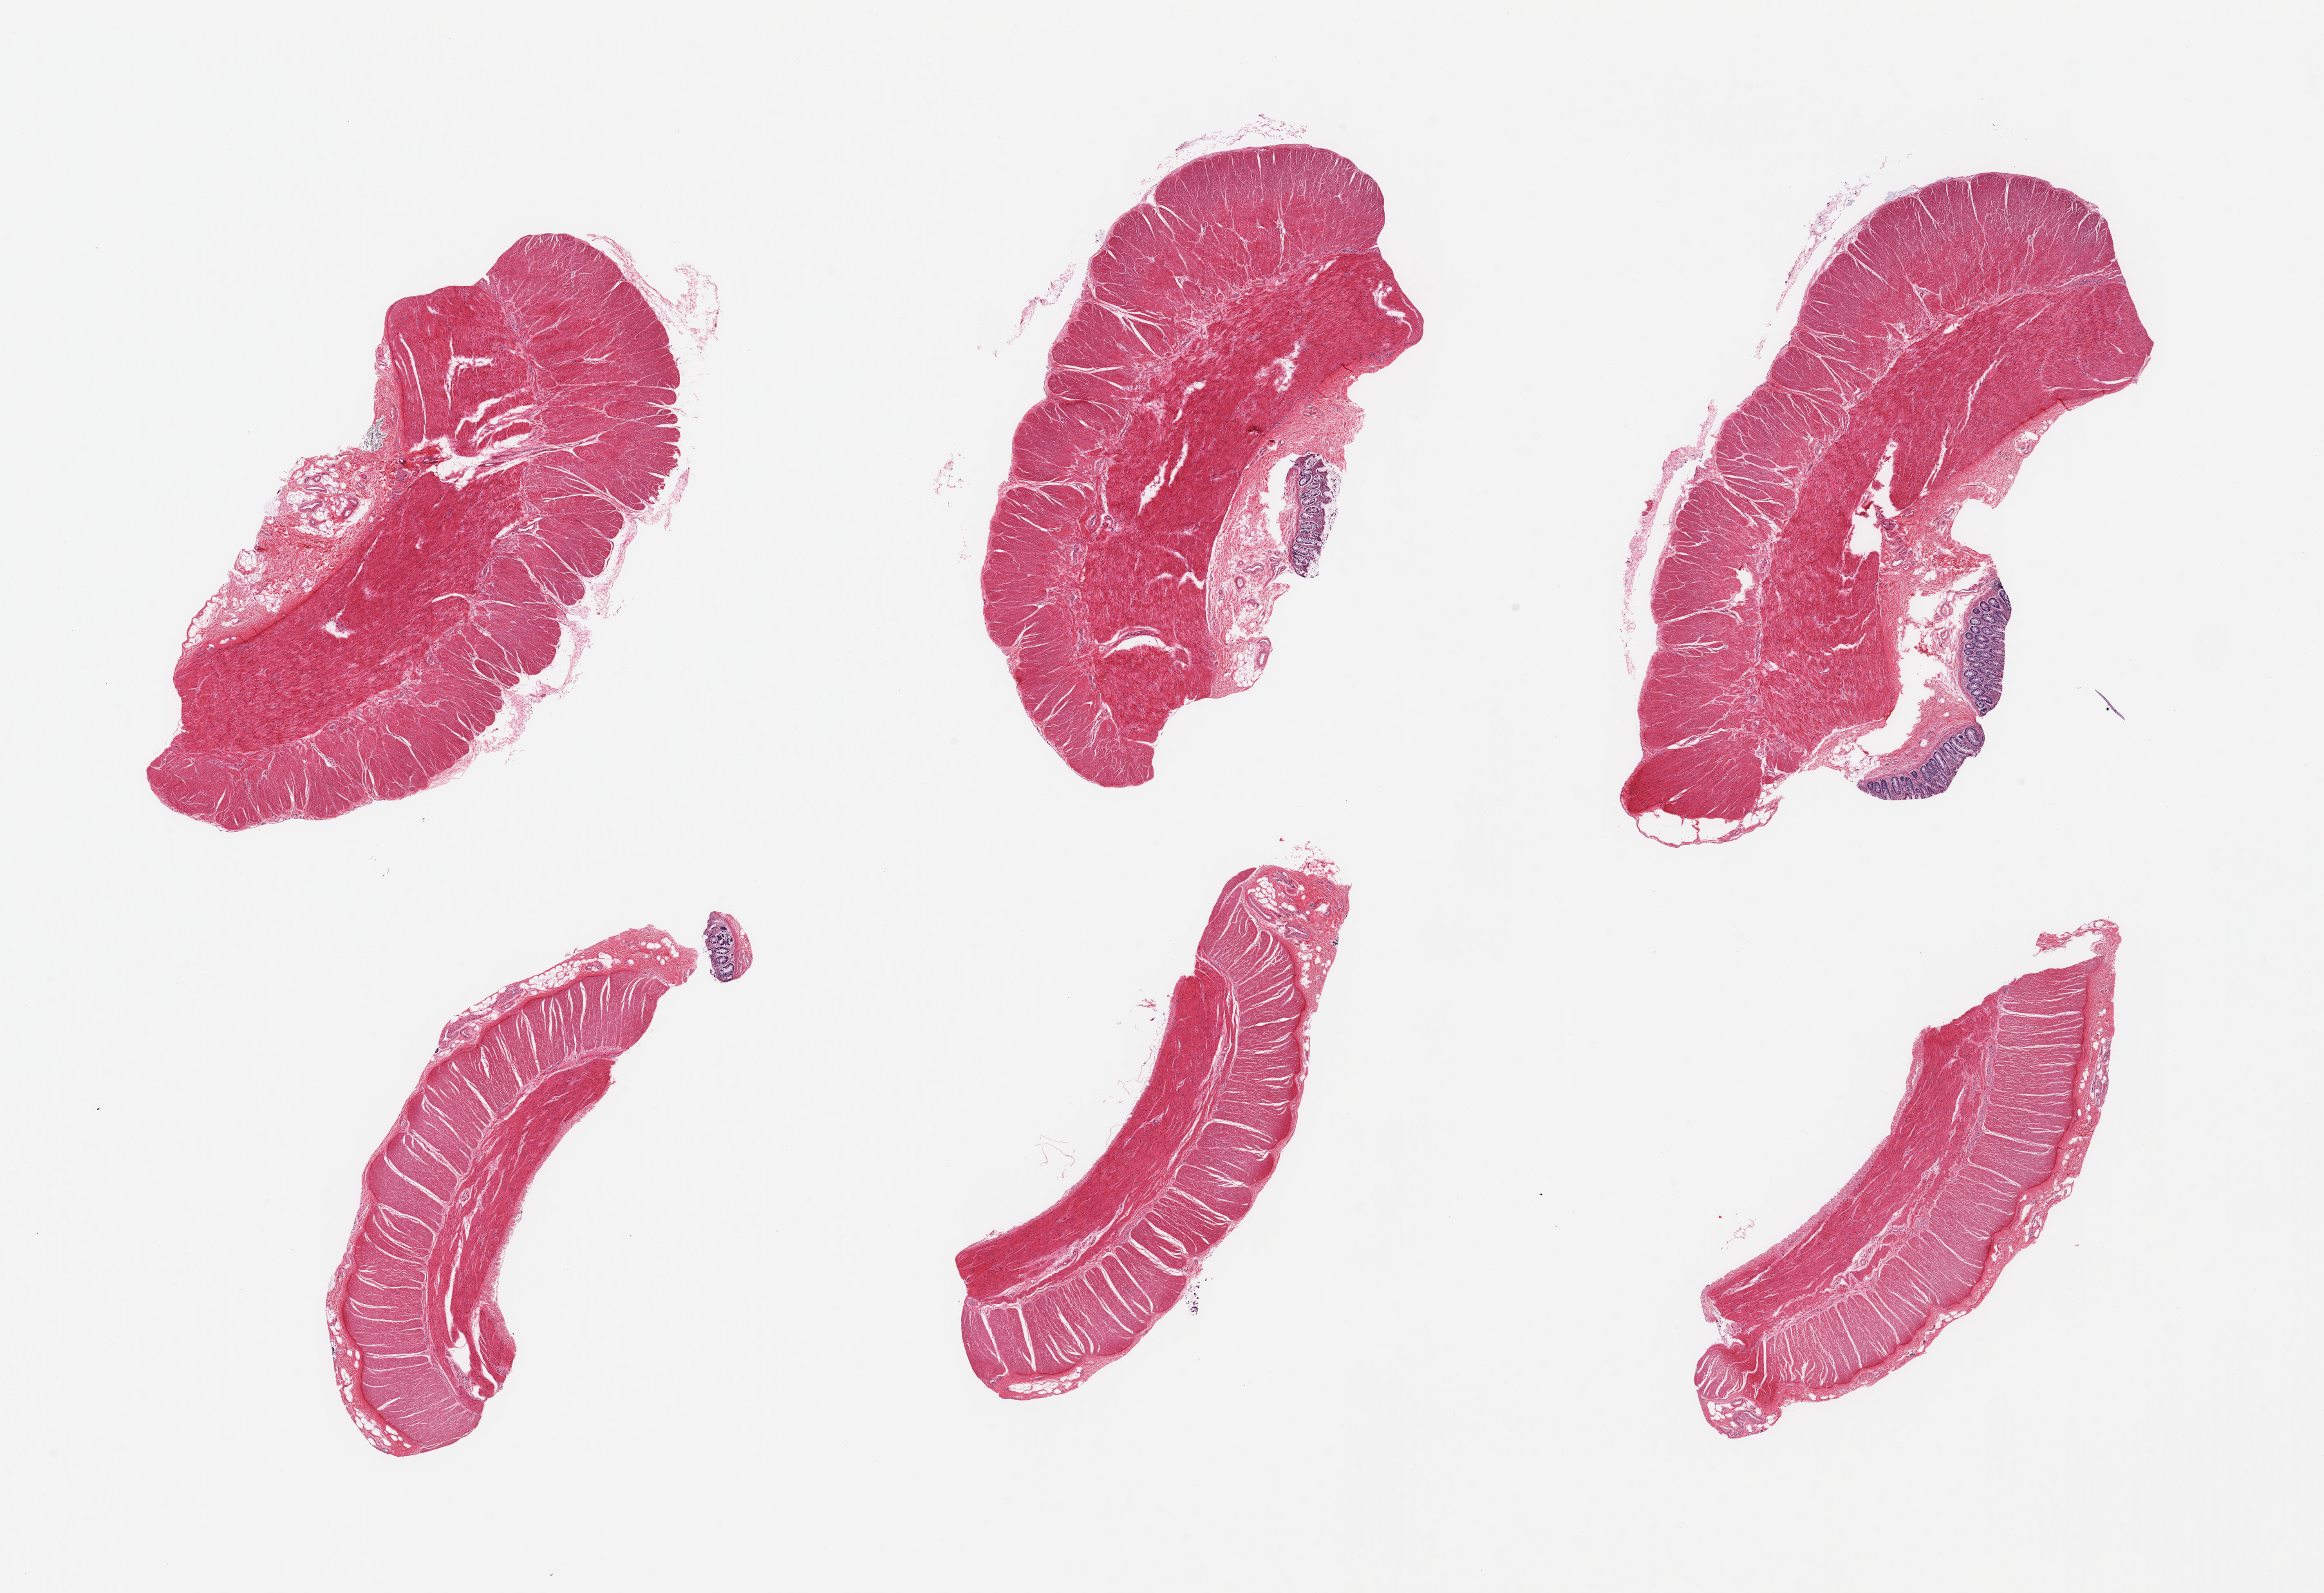
Digitized H&E-stained section — low-resolution overview of the scanned area, about 28.5 x 19.6 mm, PAXgene-fixed paraffin-embedded (PFPE) section, section of sigmoid colon (target tissue), donor tissue sample. Donor: male.
- pathologist's review note for this sample: 6 pieces; predominantly target muscularis, few strips of residual mucosa